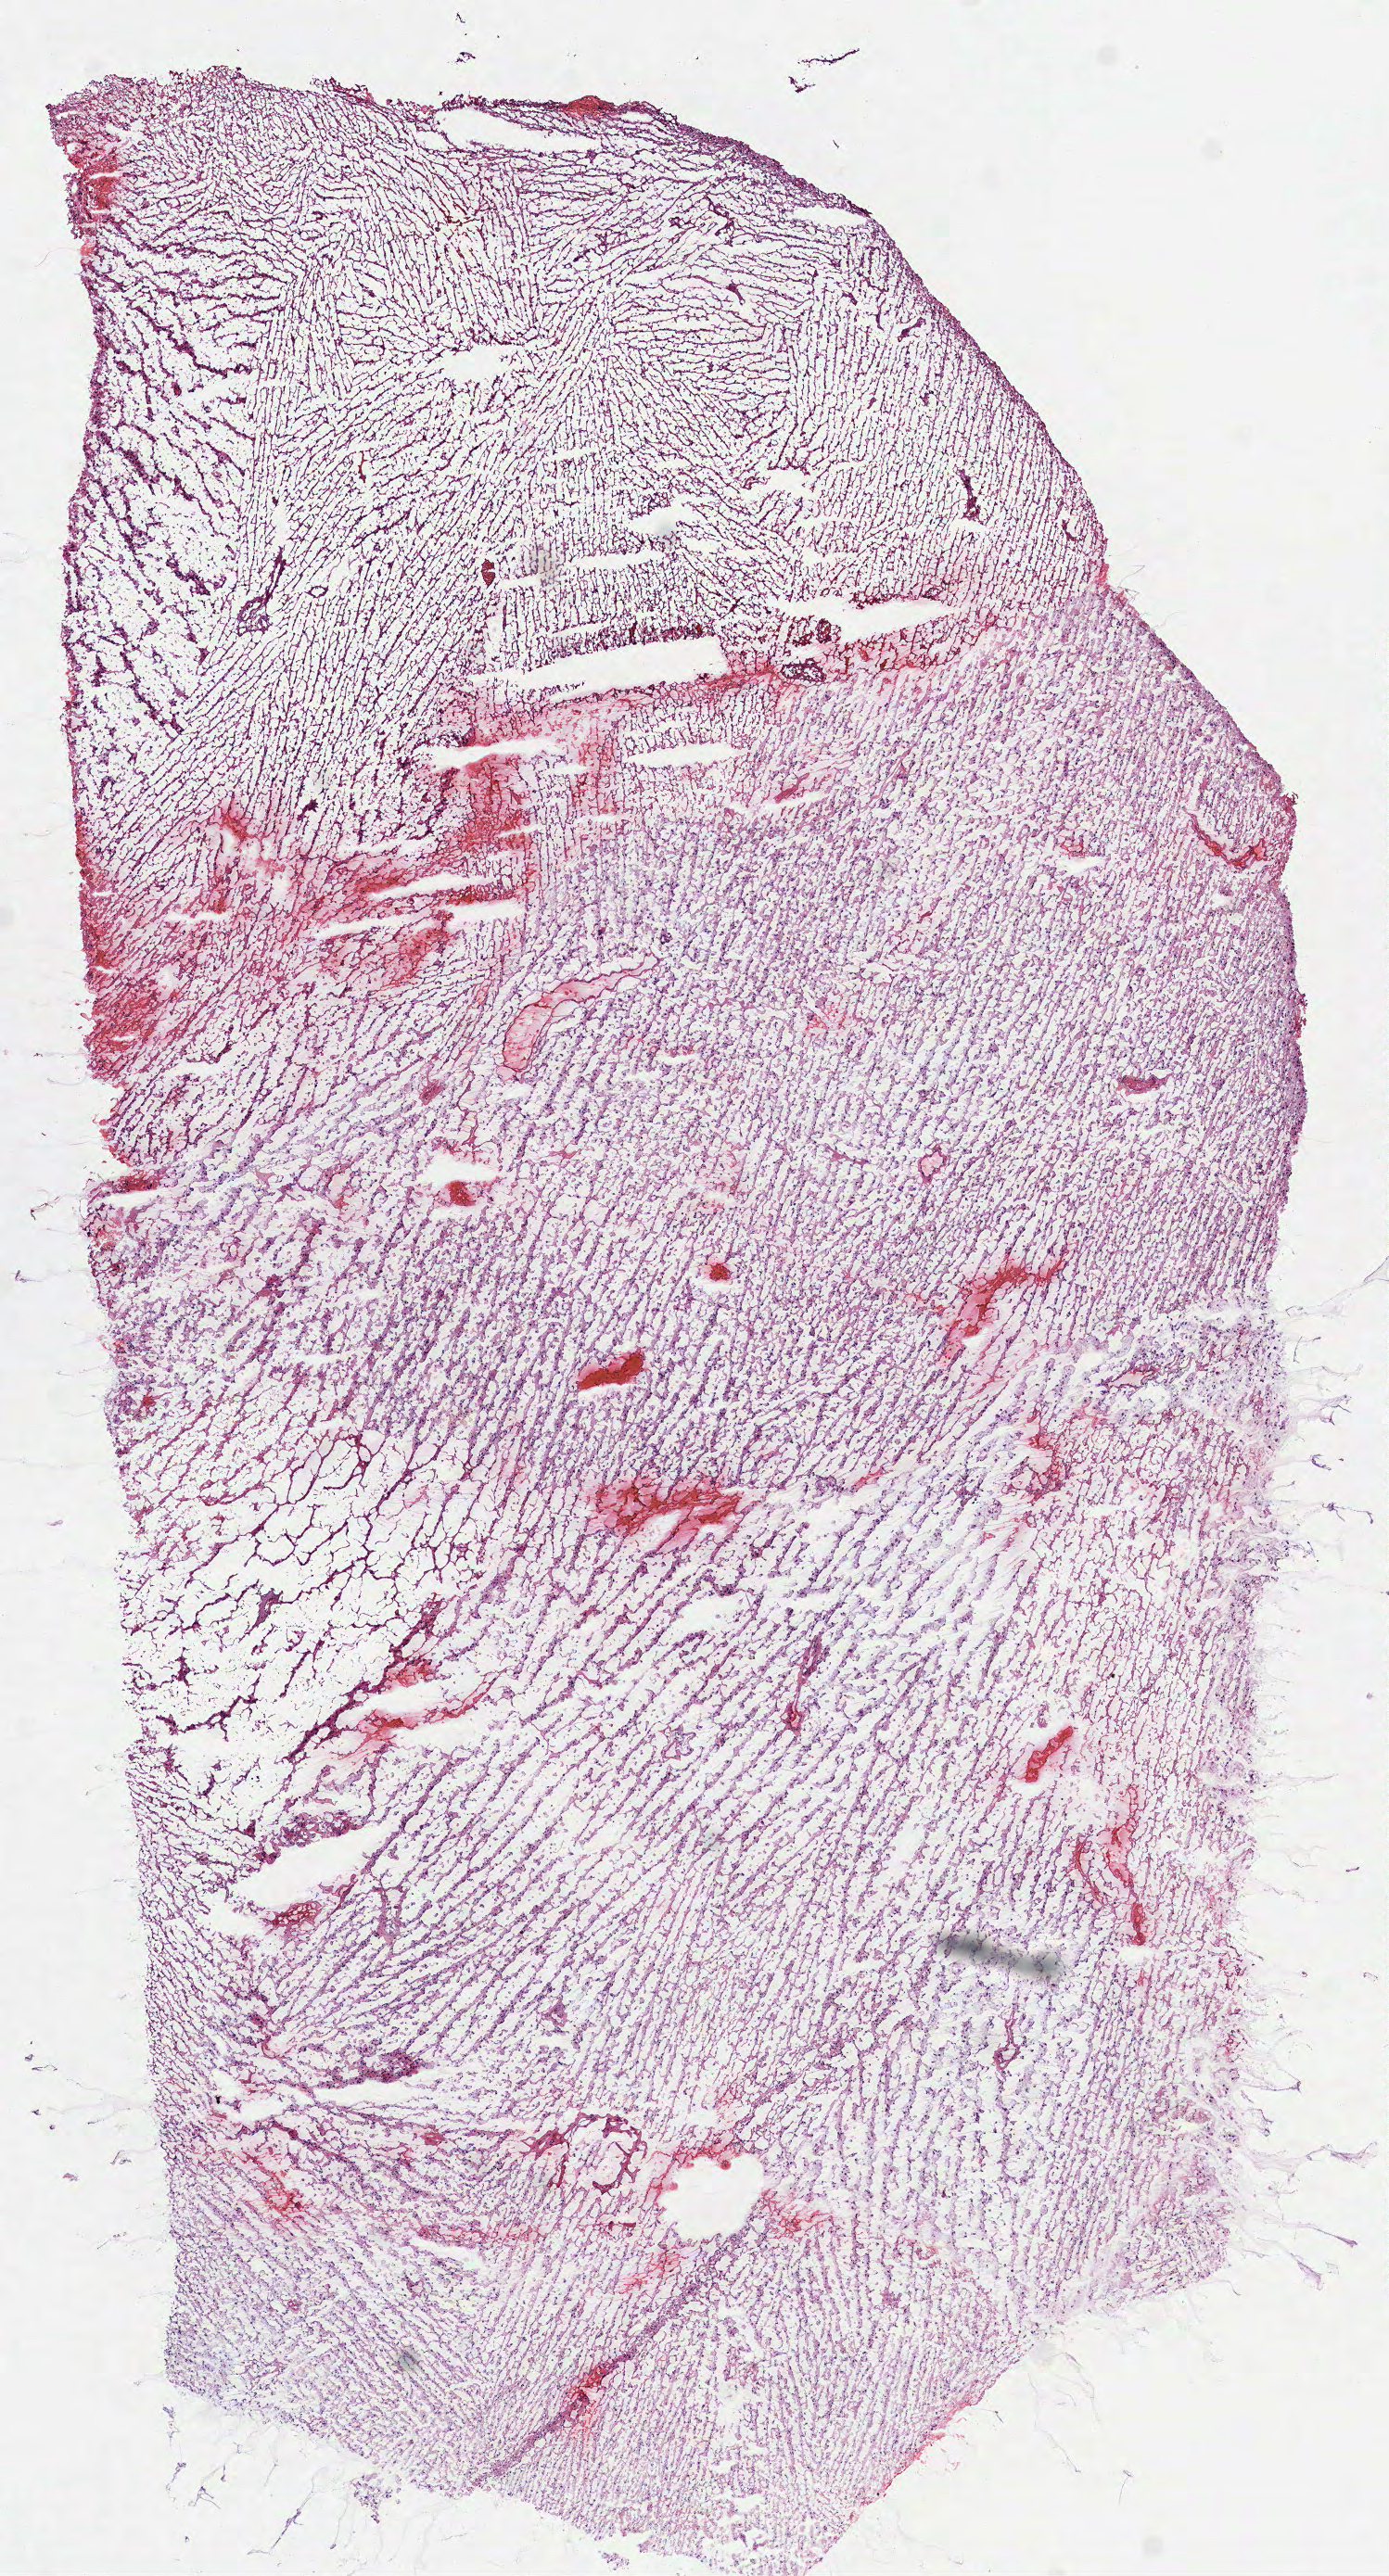
Whole-slide histology image, H&E-stained, shown as a low-resolution overview of the whole scanned area (about 6.0 x 11.2 mm, slide scanned at 40x). Frozen section from the top of the tissue portion. Sample: primary tumour, brain. Male patient; age at initial diagnosis 73 years. Pathologist review of this section (percent, as recorded): tumour cells 100%, tumour nuclei 75%.
Diagnosis: Glioblastoma.